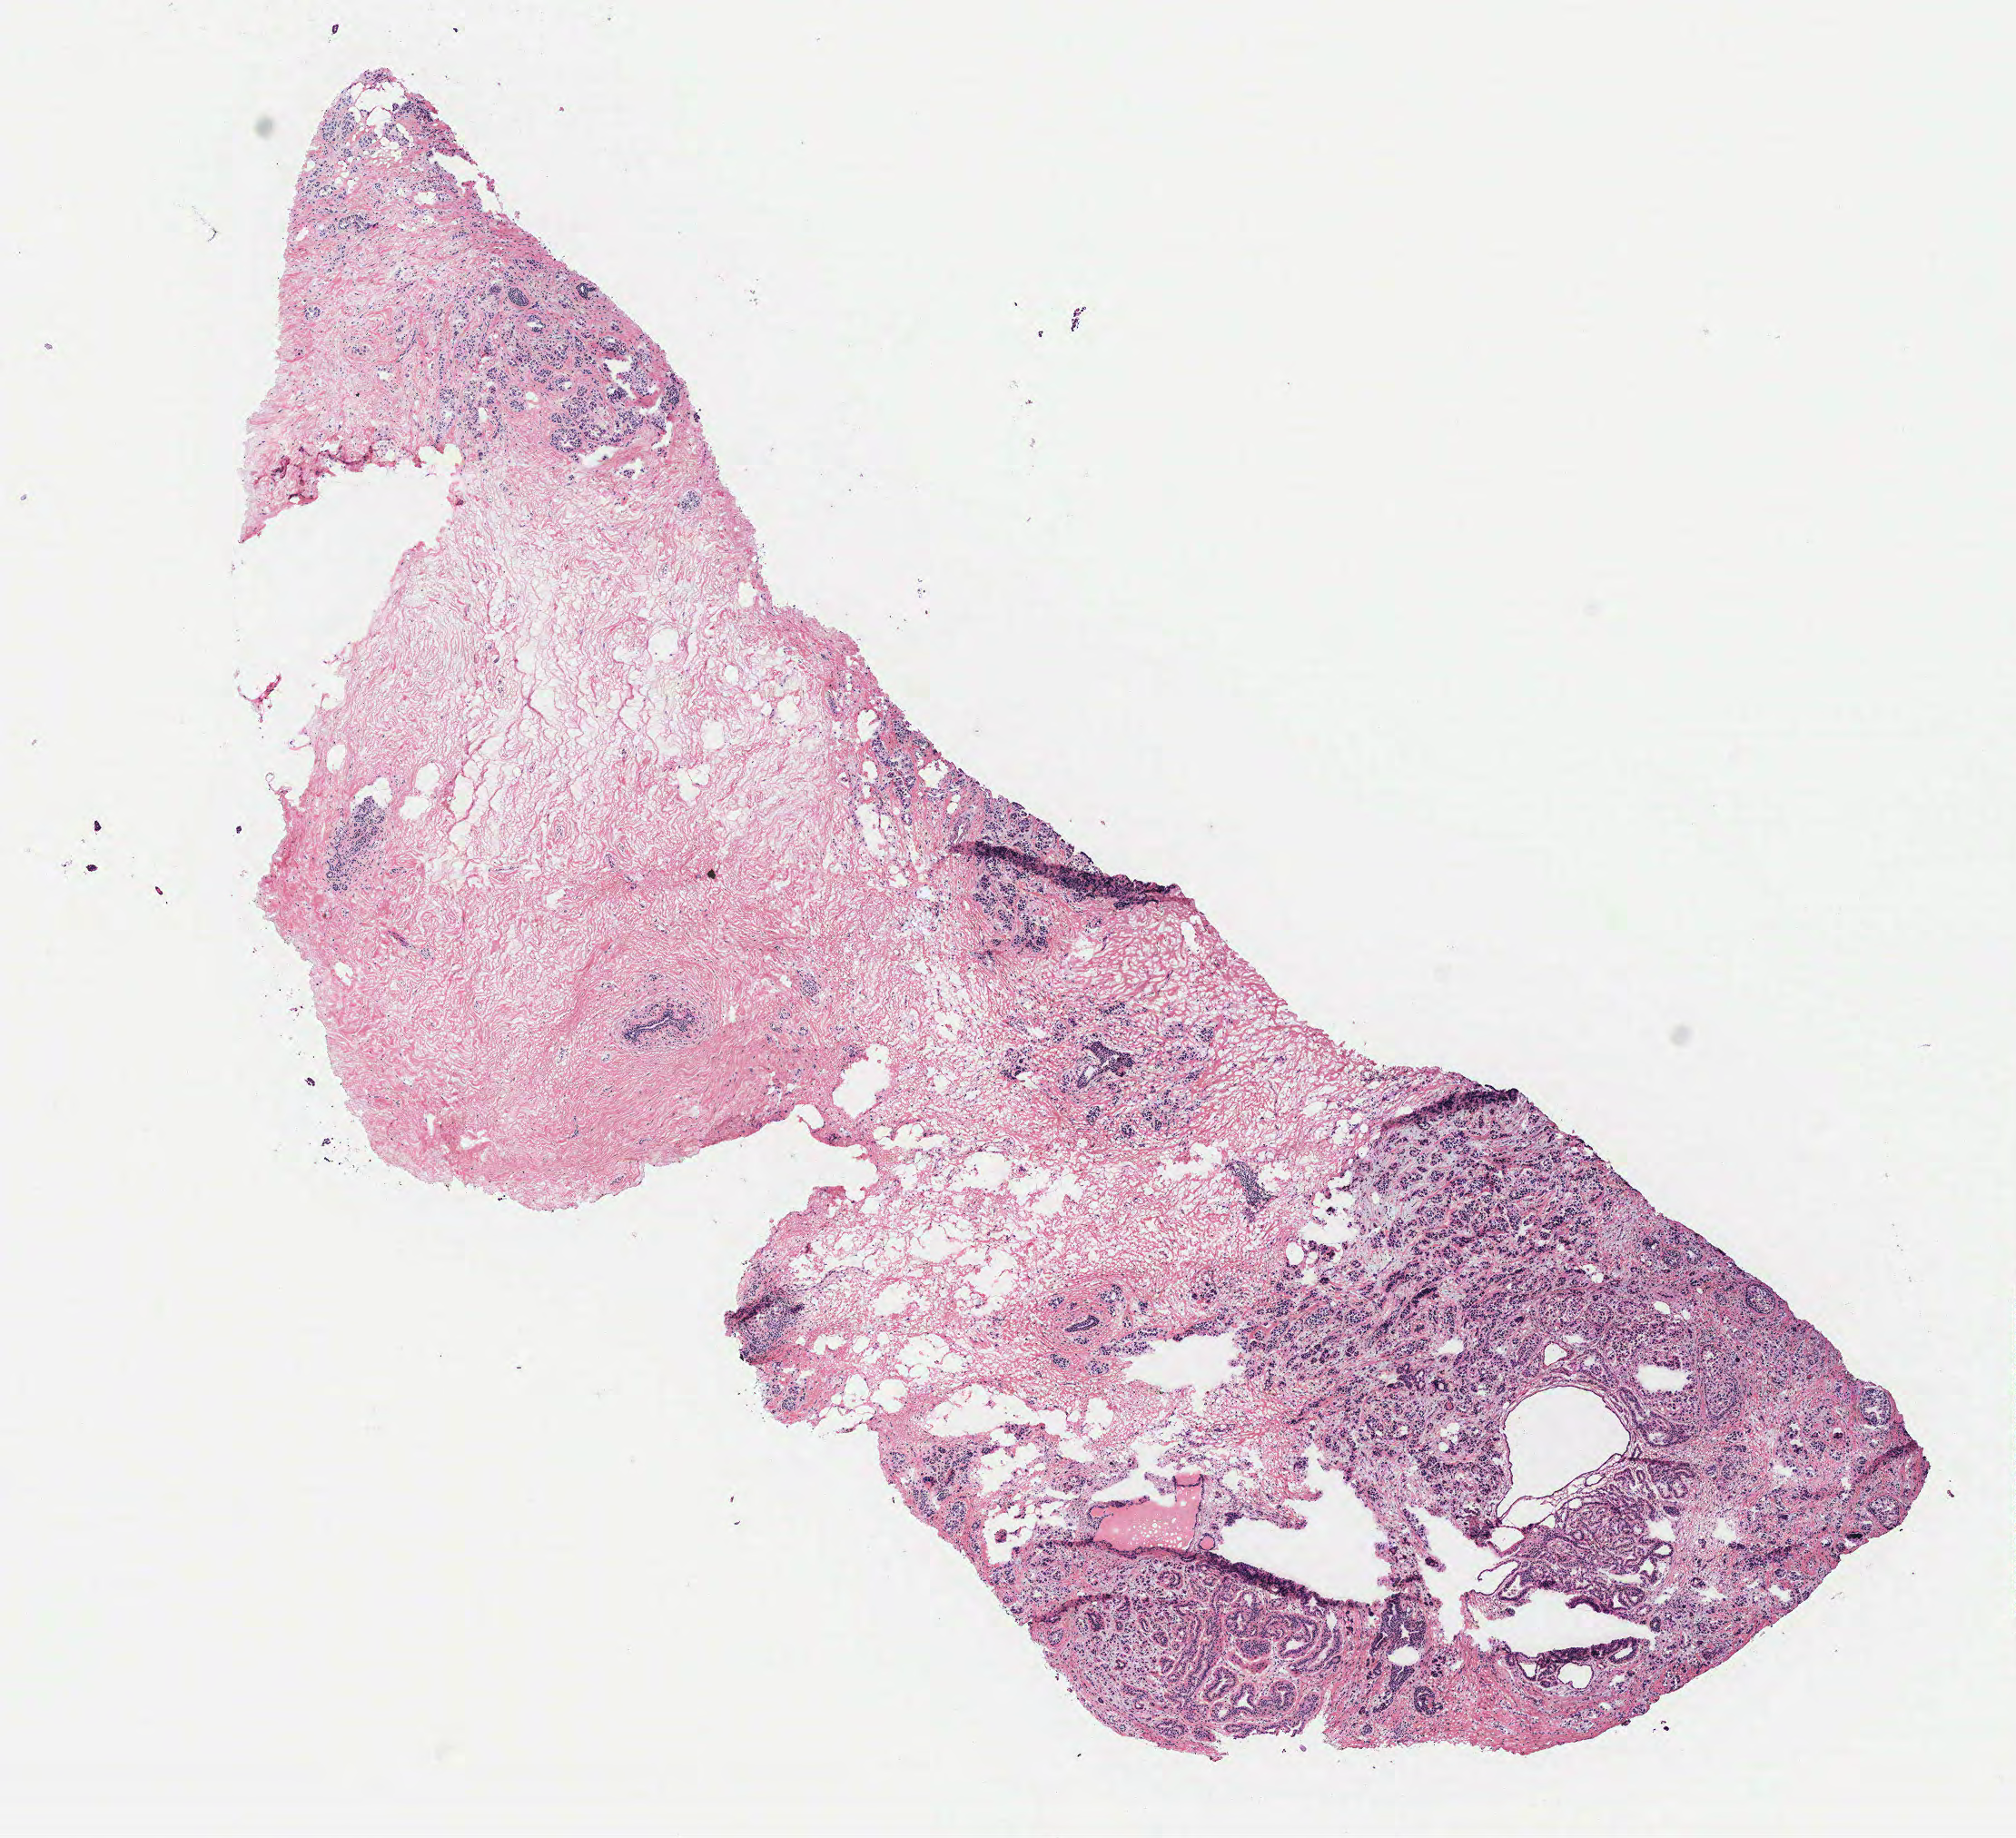
Digitized H&E-stained tissue section (whole slide) — a low-resolution overview of the entire scanned area, about 8.9 x 8.1 mm. Breast, tissue type not recorded.
* patient diagnosis (cohort enrolment): breast cancer (breast)